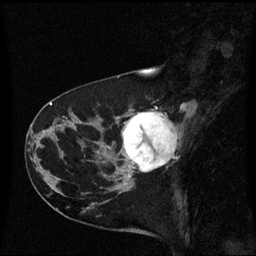
Breast MRI (dynamic contrast-enhanced), one sagittal slice. Dynamic contrast-enhanced series, image 2 of 3 at this slice position (ordered by acquisition). 1.5 T. TE 4.2 ms, TR 8.4 ms. 2 mm slice thickness. 256 × 256 image matrix, field of view 220 × 220 mm. Female patient, age 41 years. Case-level facts recorded for this patient, not image findings: setting: breast cancer imaged before/during neoadjuvant chemotherapy; receptor status: triple-negative.
Annotated regions visible in this slice (semi-automatically segmented with operator editing):
- analysis volume of interest (the breast-tissue region the enhancement analysis was run in; not a lesion): bounding box (x1, y1, x2, y2) in pixels: (116, 110, 186, 177)
- tumour enhancement mask (voxels above the 70 % enhancement threshold inside the analysis volume of interest): (122, 112, 177, 173)